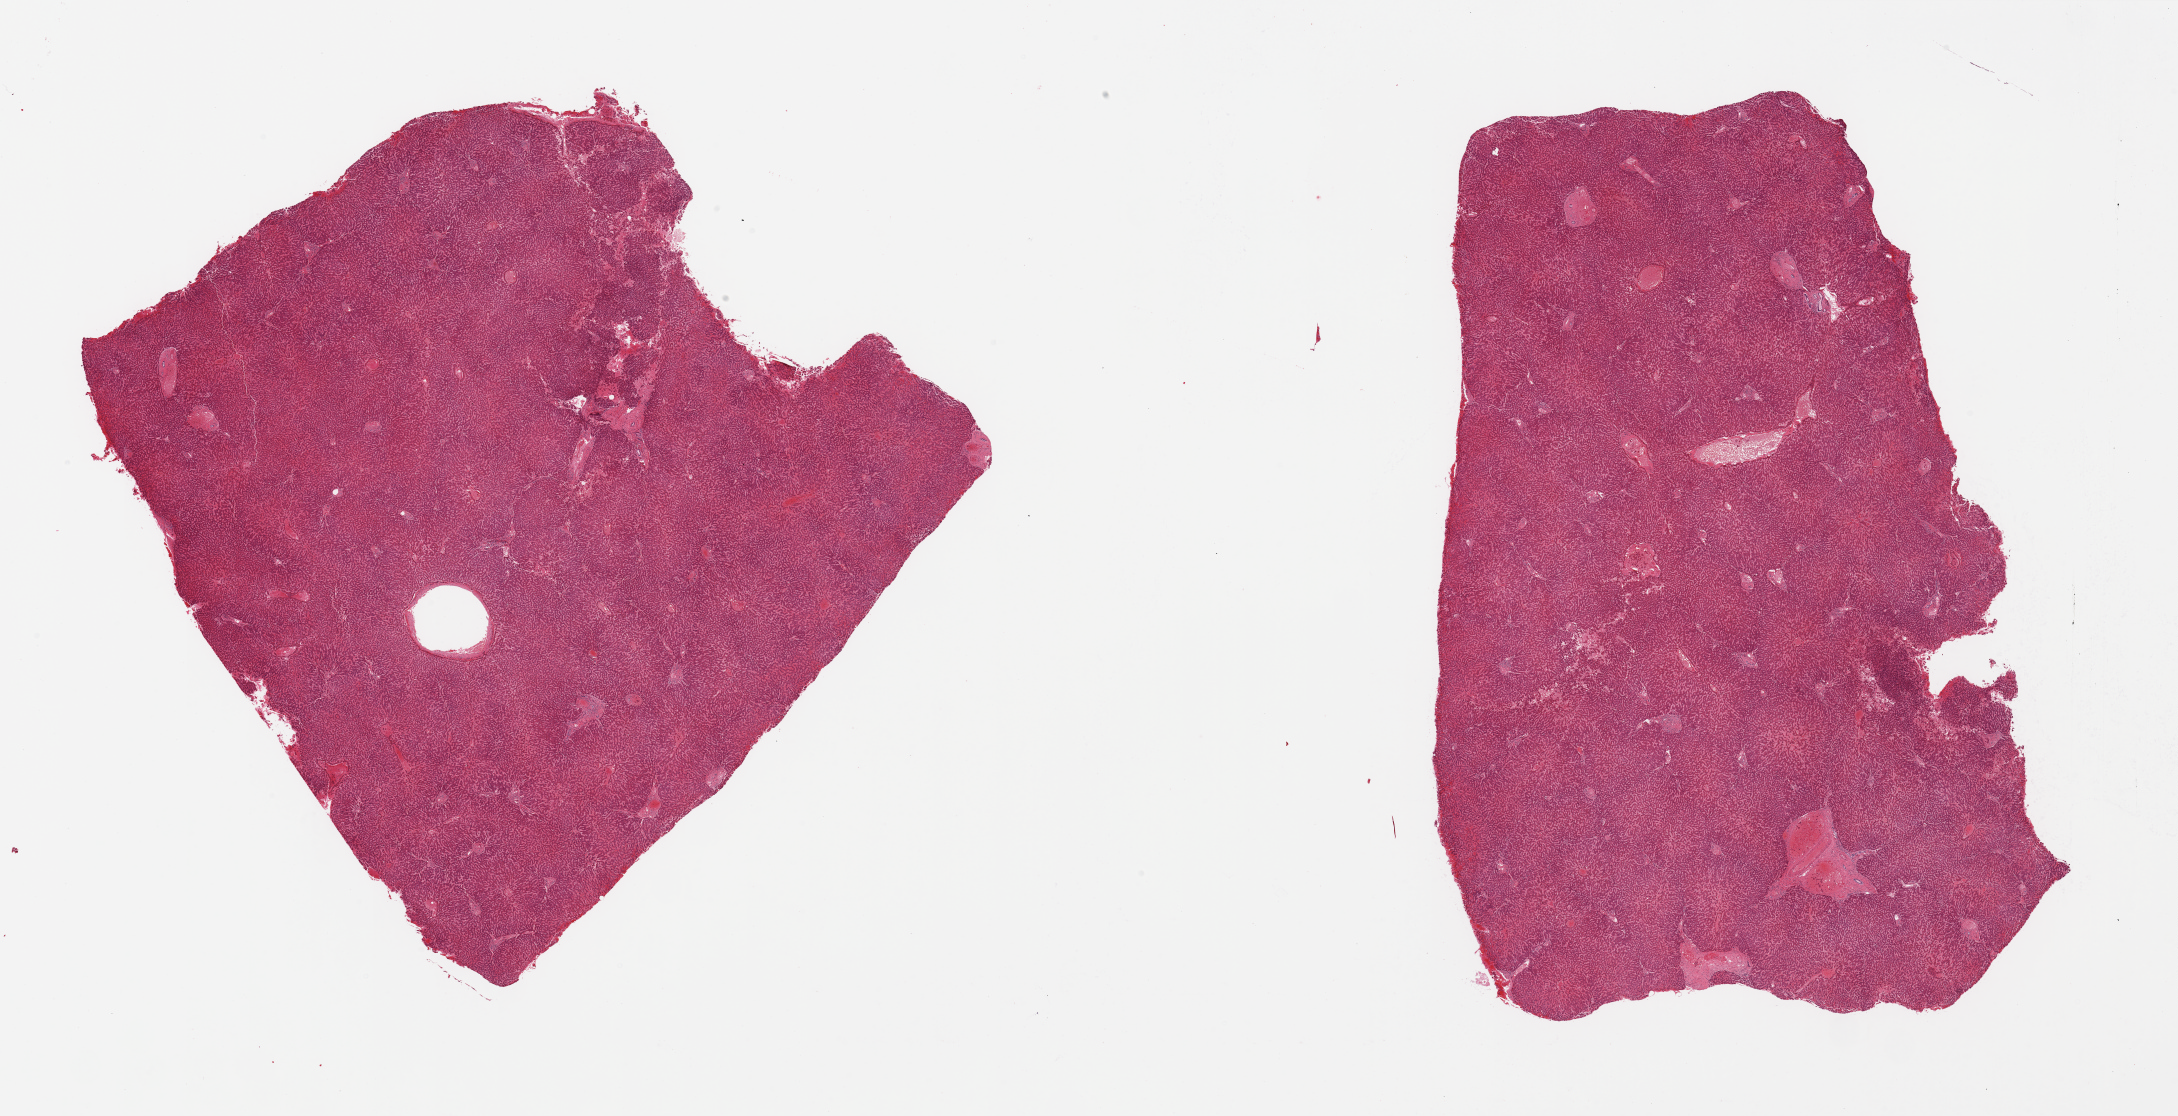
Whole-slide image, haematoxylin and eosin stain — whole scanned area (about 34.5 x 17.7 mm) shown as a low-resolution overview, PAXgene-fixed paraffin-embedded (PFPE) section, section of liver (target tissue), donor tissue sample.
Reviewer comment on this tissue sample: 2 pieces, mild congestion, no significant steatosis.